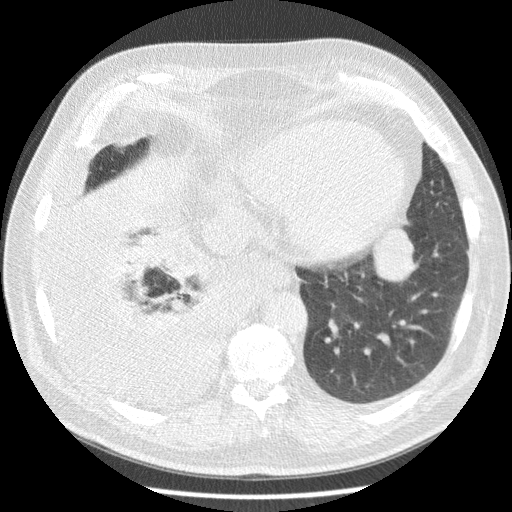
Low-dose screening chest CT, axial slice, third screening round (two years after baseline), lung window (W 1500 / L -600 HU), 2.5 mm slice thickness, slice 59 of 180 in the series, 512 × 512 image matrix. Male participant, aged 63 years at enrolment.
- Lesion marked by an expert reader, bounding box <352,223,418,292> (left, top, right, bottom; pixels).
- Screening reader's record for this exam (one nodule recorded; not confirmed to be the boxed lesion): non-calcified nodule or mass ≥4 mm, left lower lobe, 34 × 31 mm, smooth margins, soft tissue attenuation, pre-existing on the prior screen: yes; interval growth: yes.
- Official screen result: positive, other.
- Lung cancer was diagnosed 30 days after this screen: squamous cell carcinoma, NOS, left lower lobe, stage IB (AJCC 6th edition), 48 mm at pathology.